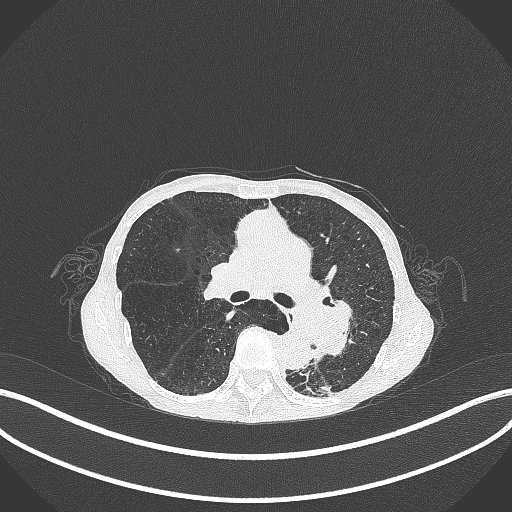
Chest CT, one axial slice; position 166 of 347 along the scan axis; lung window (W 1500 / L -600 HU); 1 mm slice thickness; 512 × 512 image matrix, field of view 400 × 400 mm. Female patient, age 70 years. Case-level facts recorded for this patient, not image findings: clinical TNM (as recorded): T3 N0 M0.
Annotated regions visible in this slice (bounding box drawn by a radiologist):
- lung tumour (recorded histology: small cell carcinoma): bounding box (x1, y1, x2, y2) in pixels: (292, 300, 367, 364)